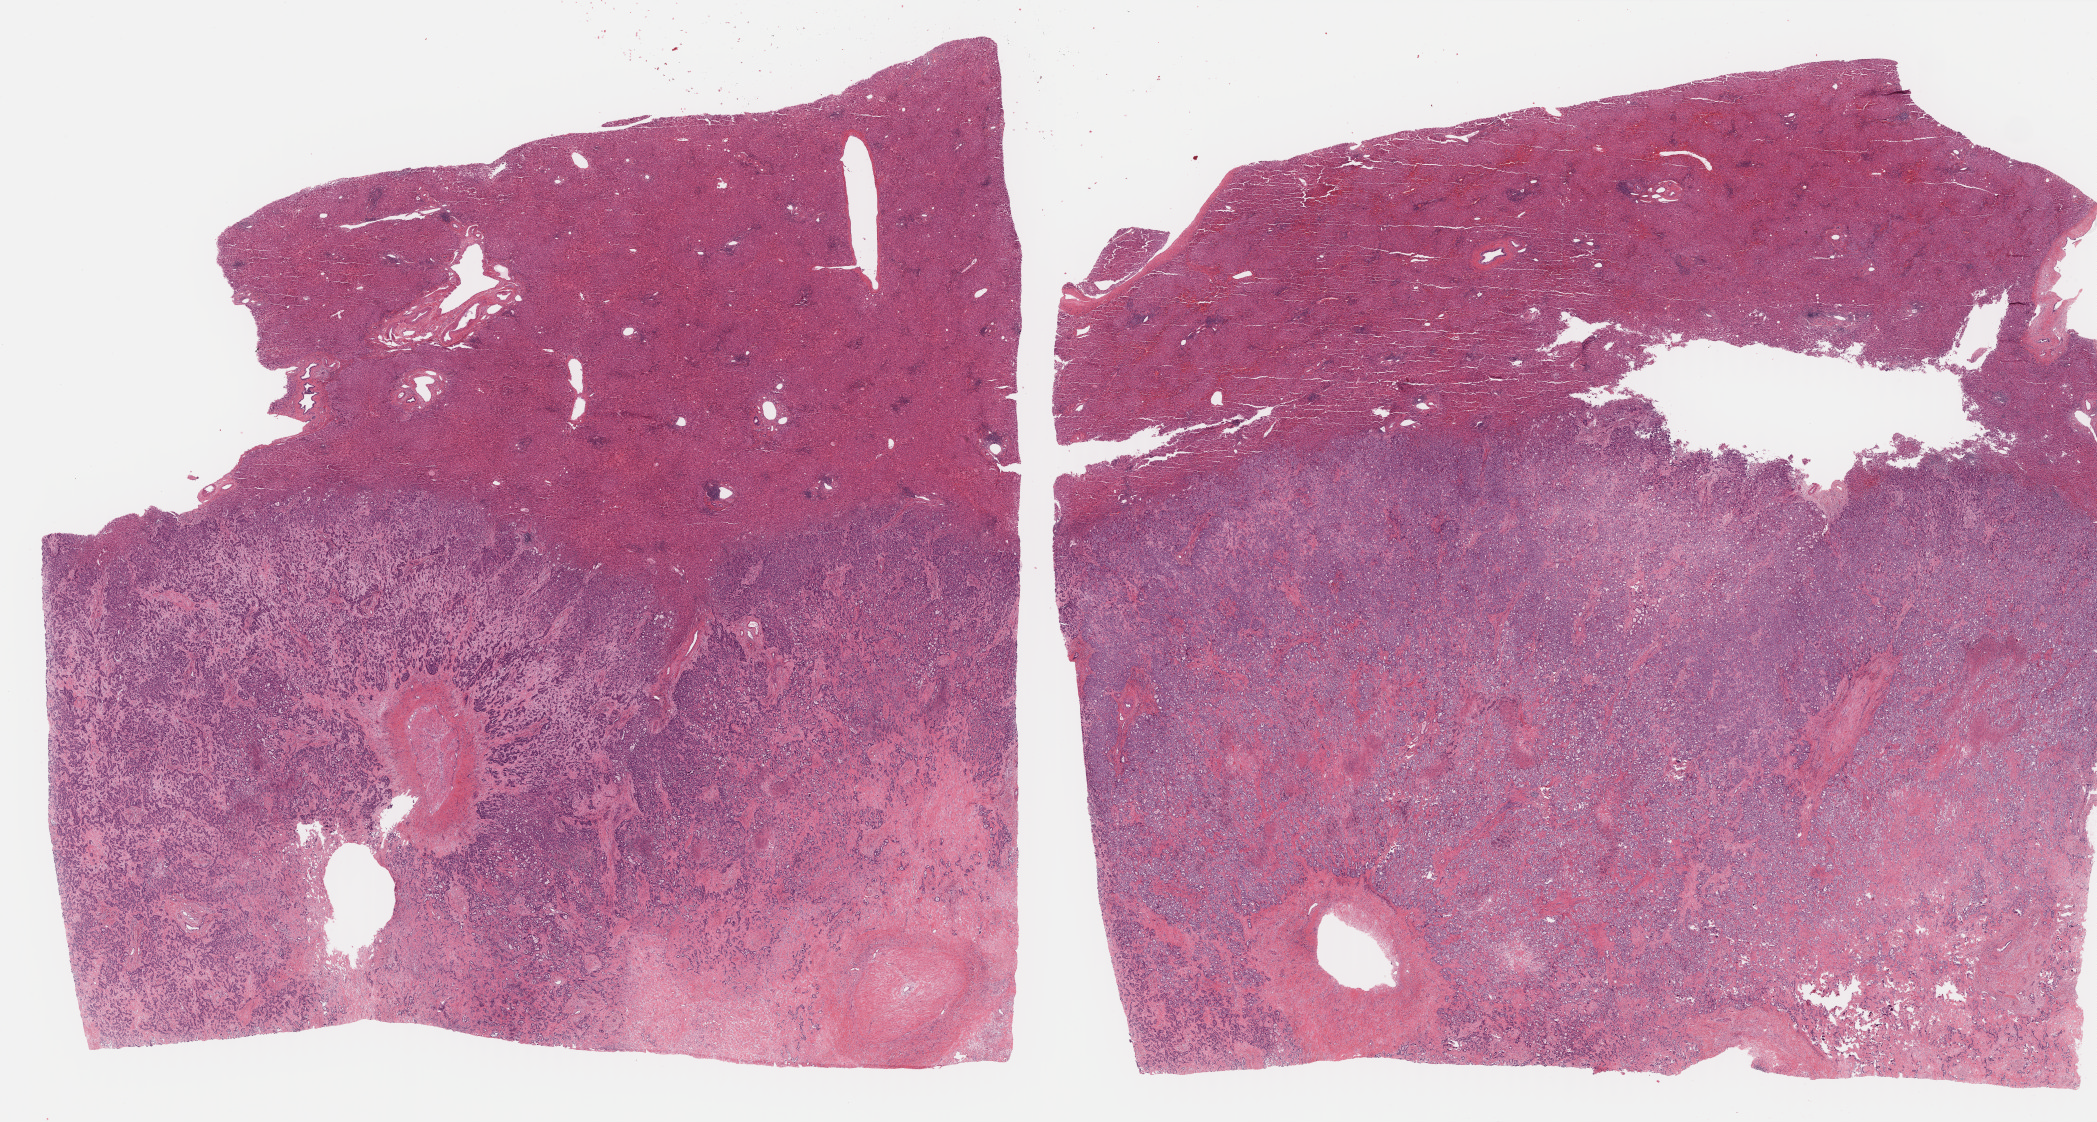
H&E whole-slide image — low-resolution overview of the scanned area, about 33.9 x 18.2 mm (slide scanned at 40x). Formalin-fixed paraffin-embedded (FFPE) diagnostic section. Bile duct, primary tumour sample. Male patient; age at initial diagnosis 68 years. Histologic grade: G2 (moderately differentiated).
• AJCC pathologic stage: II (6th edition)
• diagnosis: Cholangiocarcinoma (intrahepatic bile duct)